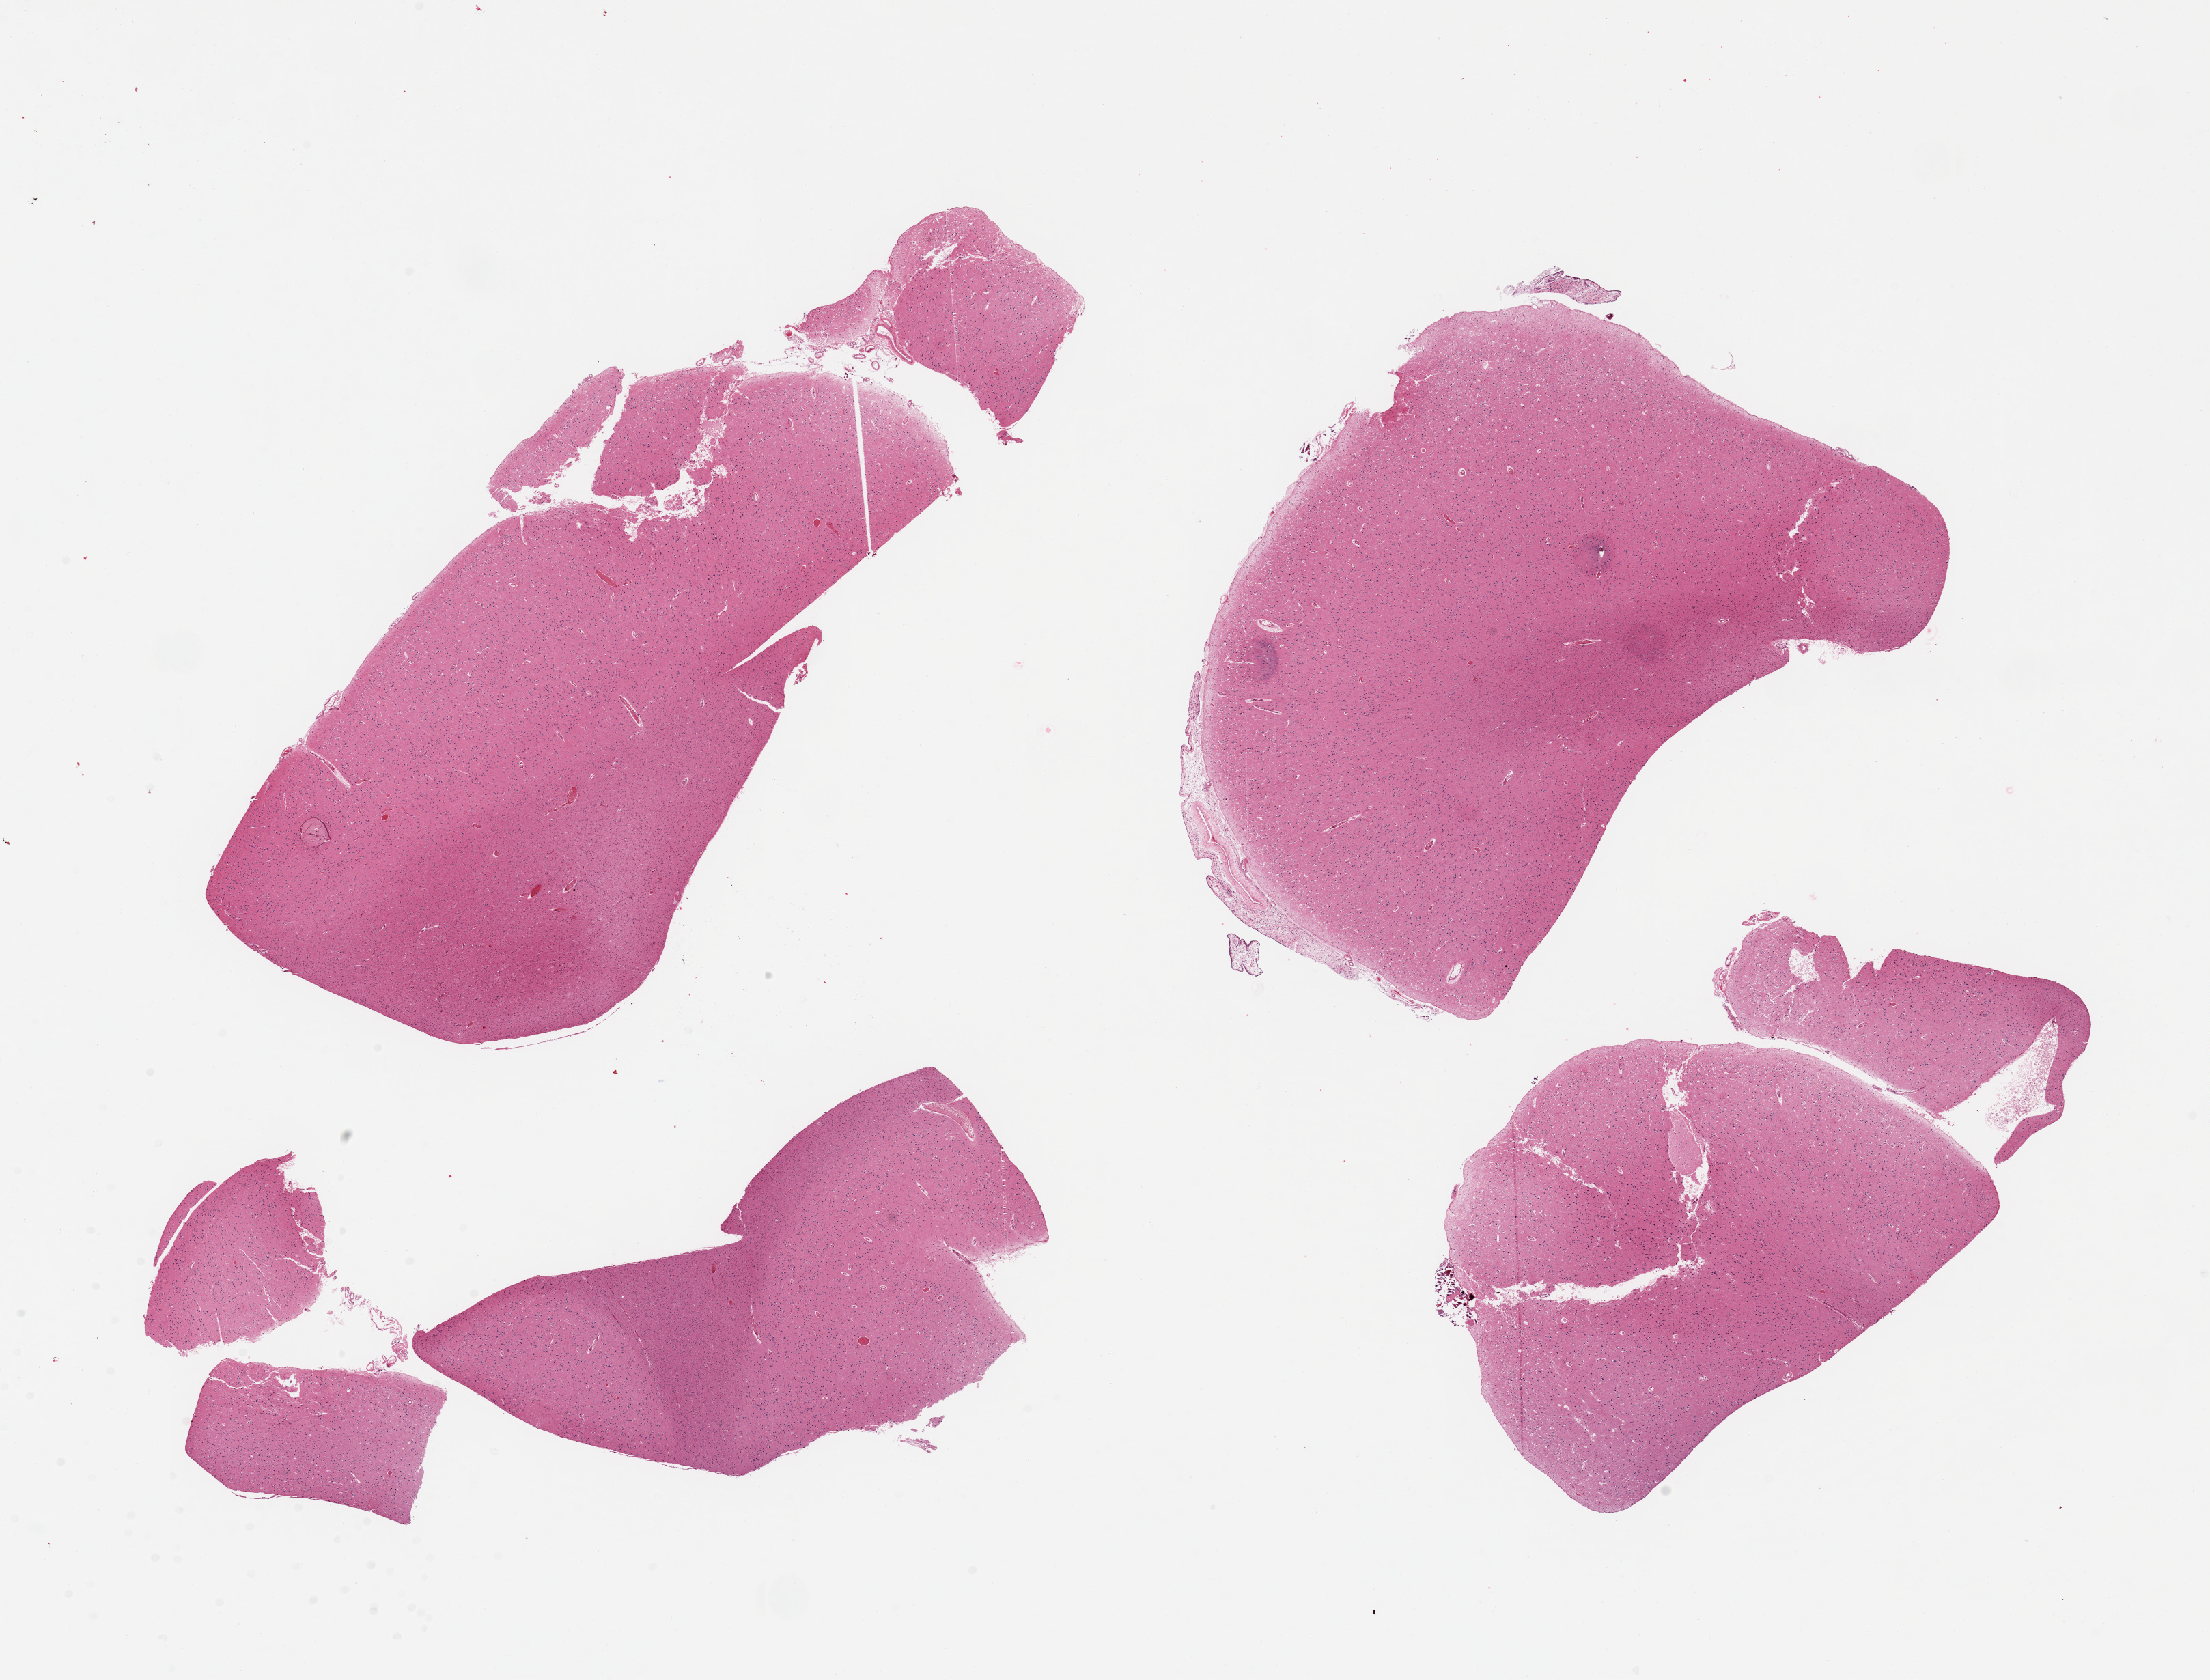
Digitized H&E-stained section, a low-resolution overview of the entire scanned area, about 25.6 x 19.5 mm (slide scanned at 20x), PAXgene-fixed paraffin-embedded (PFPE) section, target tissue: cerebral cortex, tissue donor sample. Donor sex: male.
* reviewer comment on this tissue sample: 4 fragmented pieces; focus of meninges